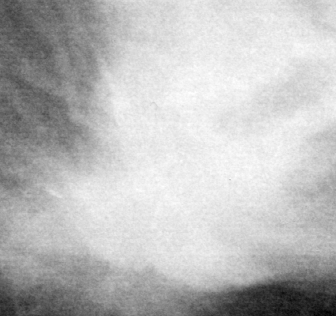
Crop from a digitized film mammogram around one marked abnormality, left breast, MLO view, BI-RADS breast density category 3 (scale 1–4).
Finding: mass, shape lobulated, margins spiculated; BI-RADS assessment category 5; subtlety rating 5 on a 1 (subtle) to 5 (obvious) scale; pathology (as recorded): malignant.